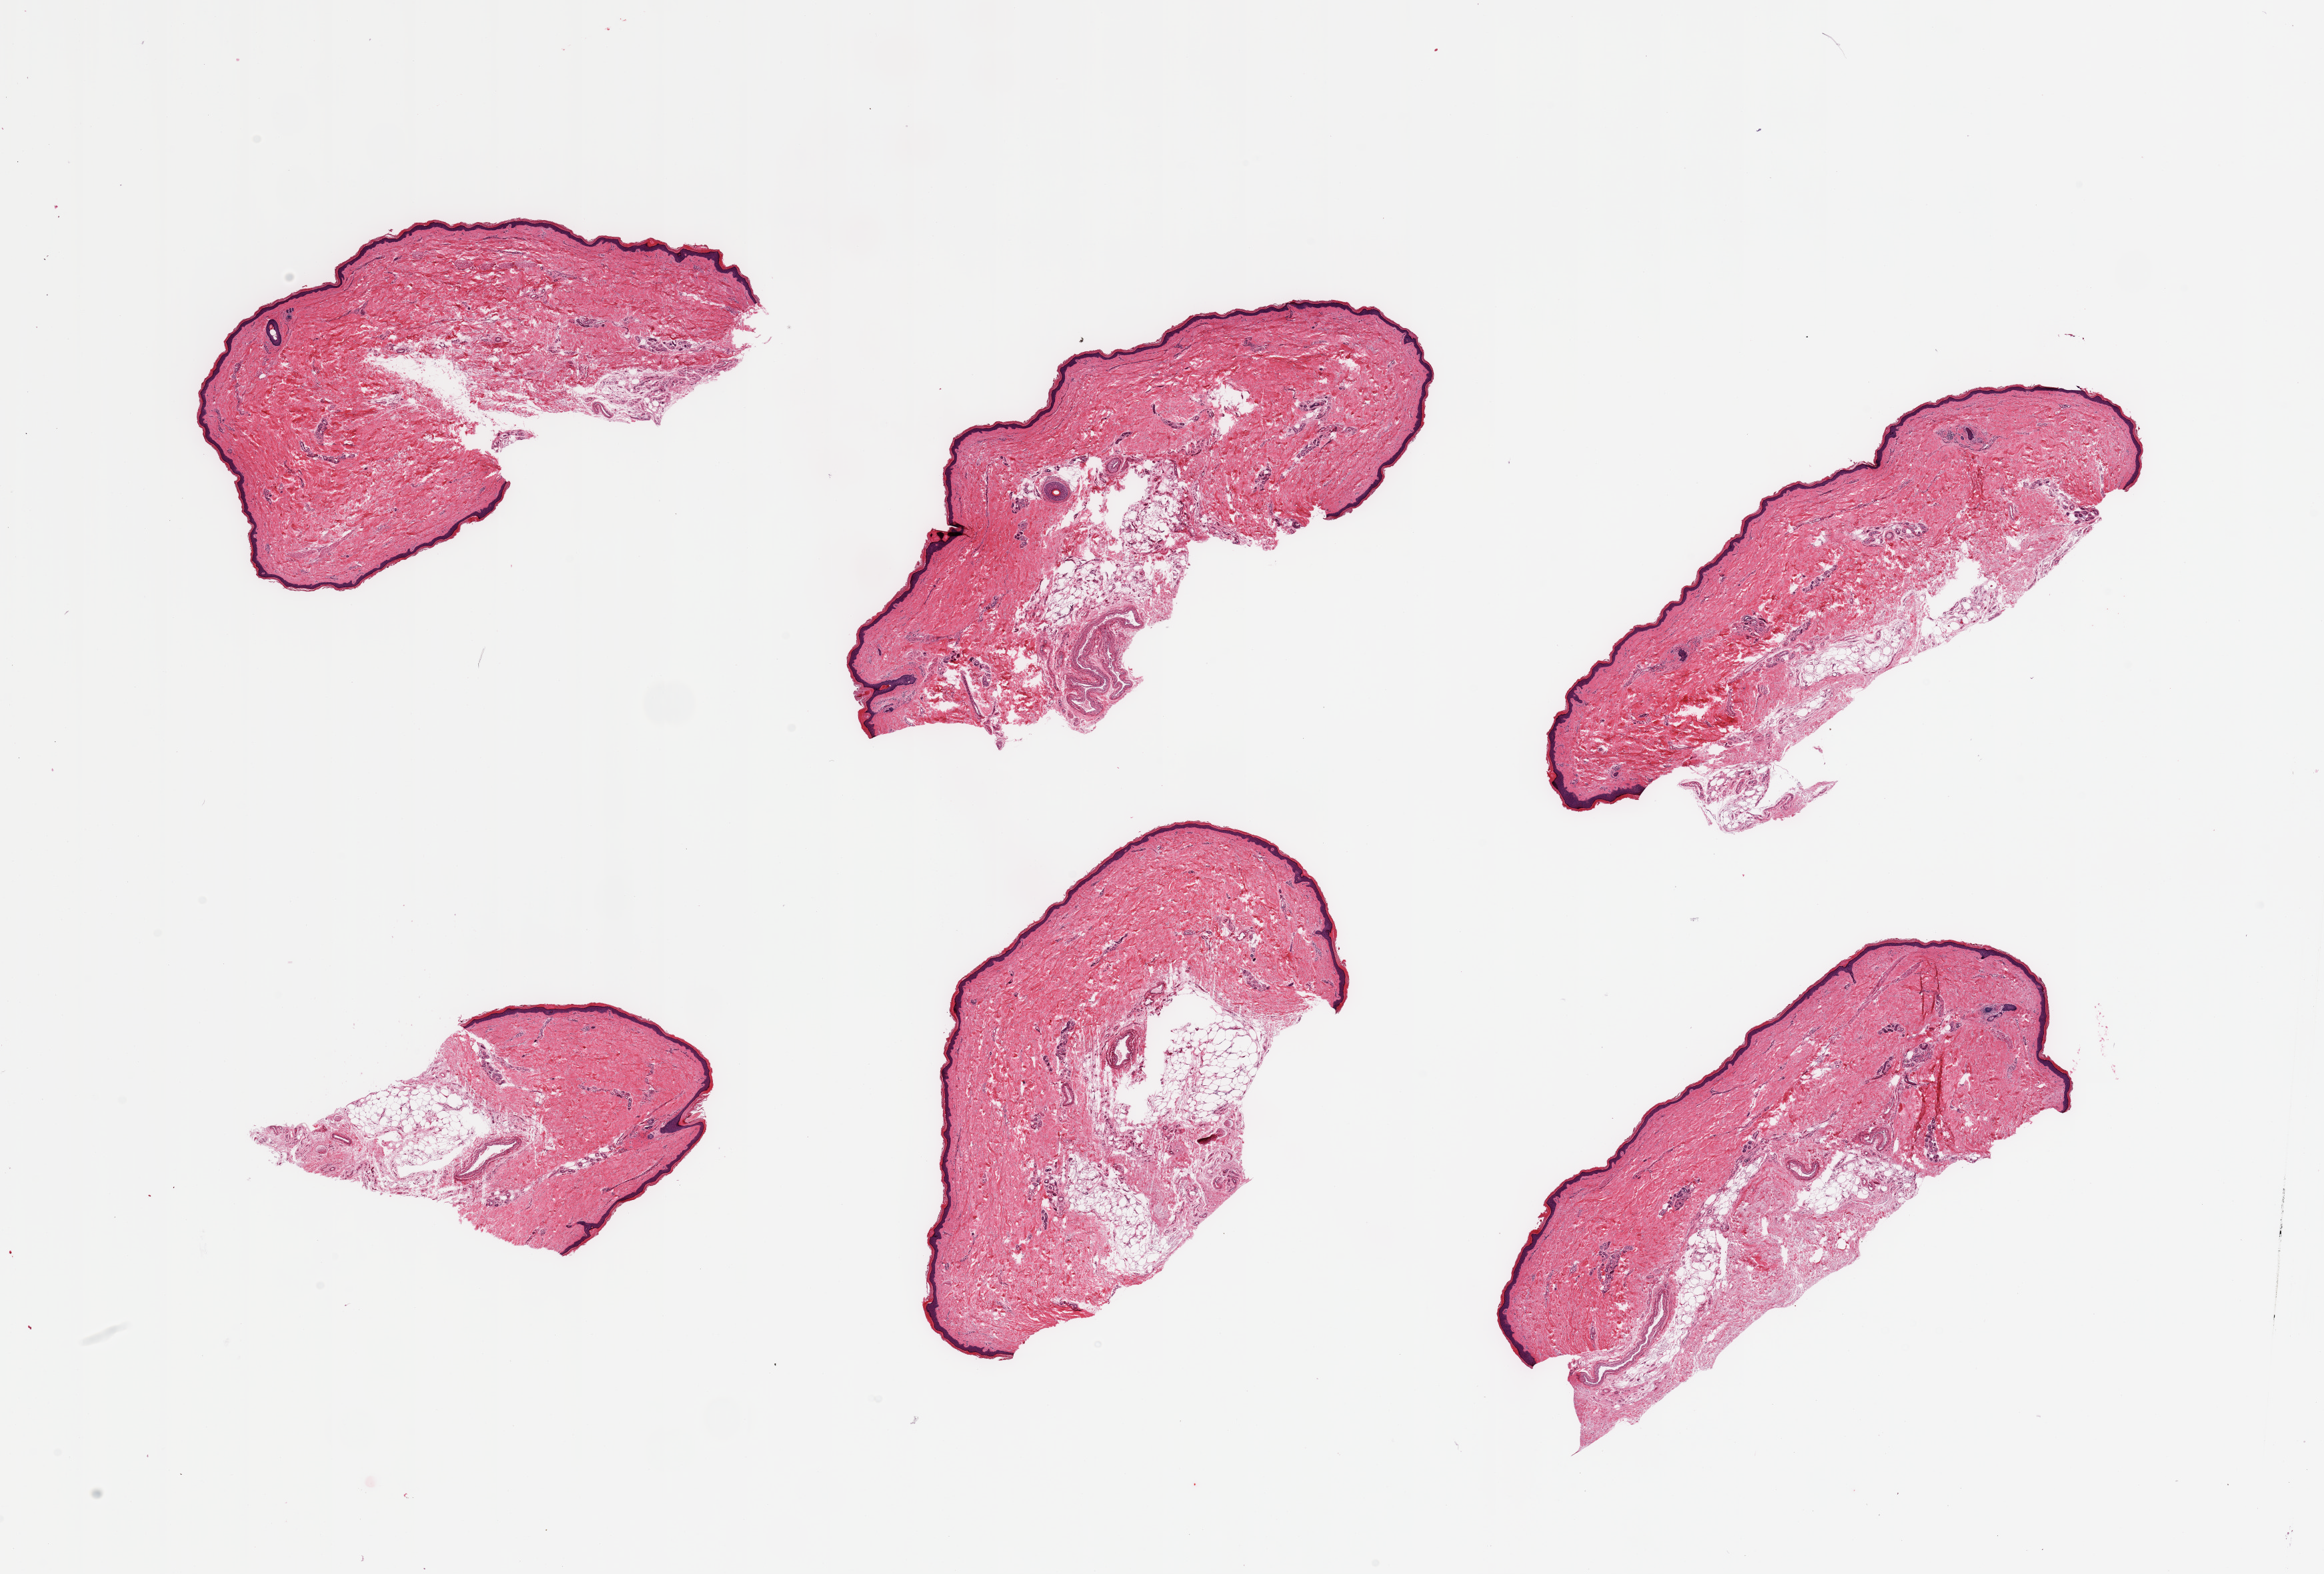
Haematoxylin and eosin whole-slide image, low-resolution overview of the scanned area, about 27.6 x 18.7 mm; PAXgene-fixed, paraffin-embedded tissue; section of skin of lower leg (target tissue); donor tissue sample.
* pathologist's review note for this sample: 6 pieces; relatively well trimmed, include up to ~10% mostly internal fat, epidermis measures 44 microns